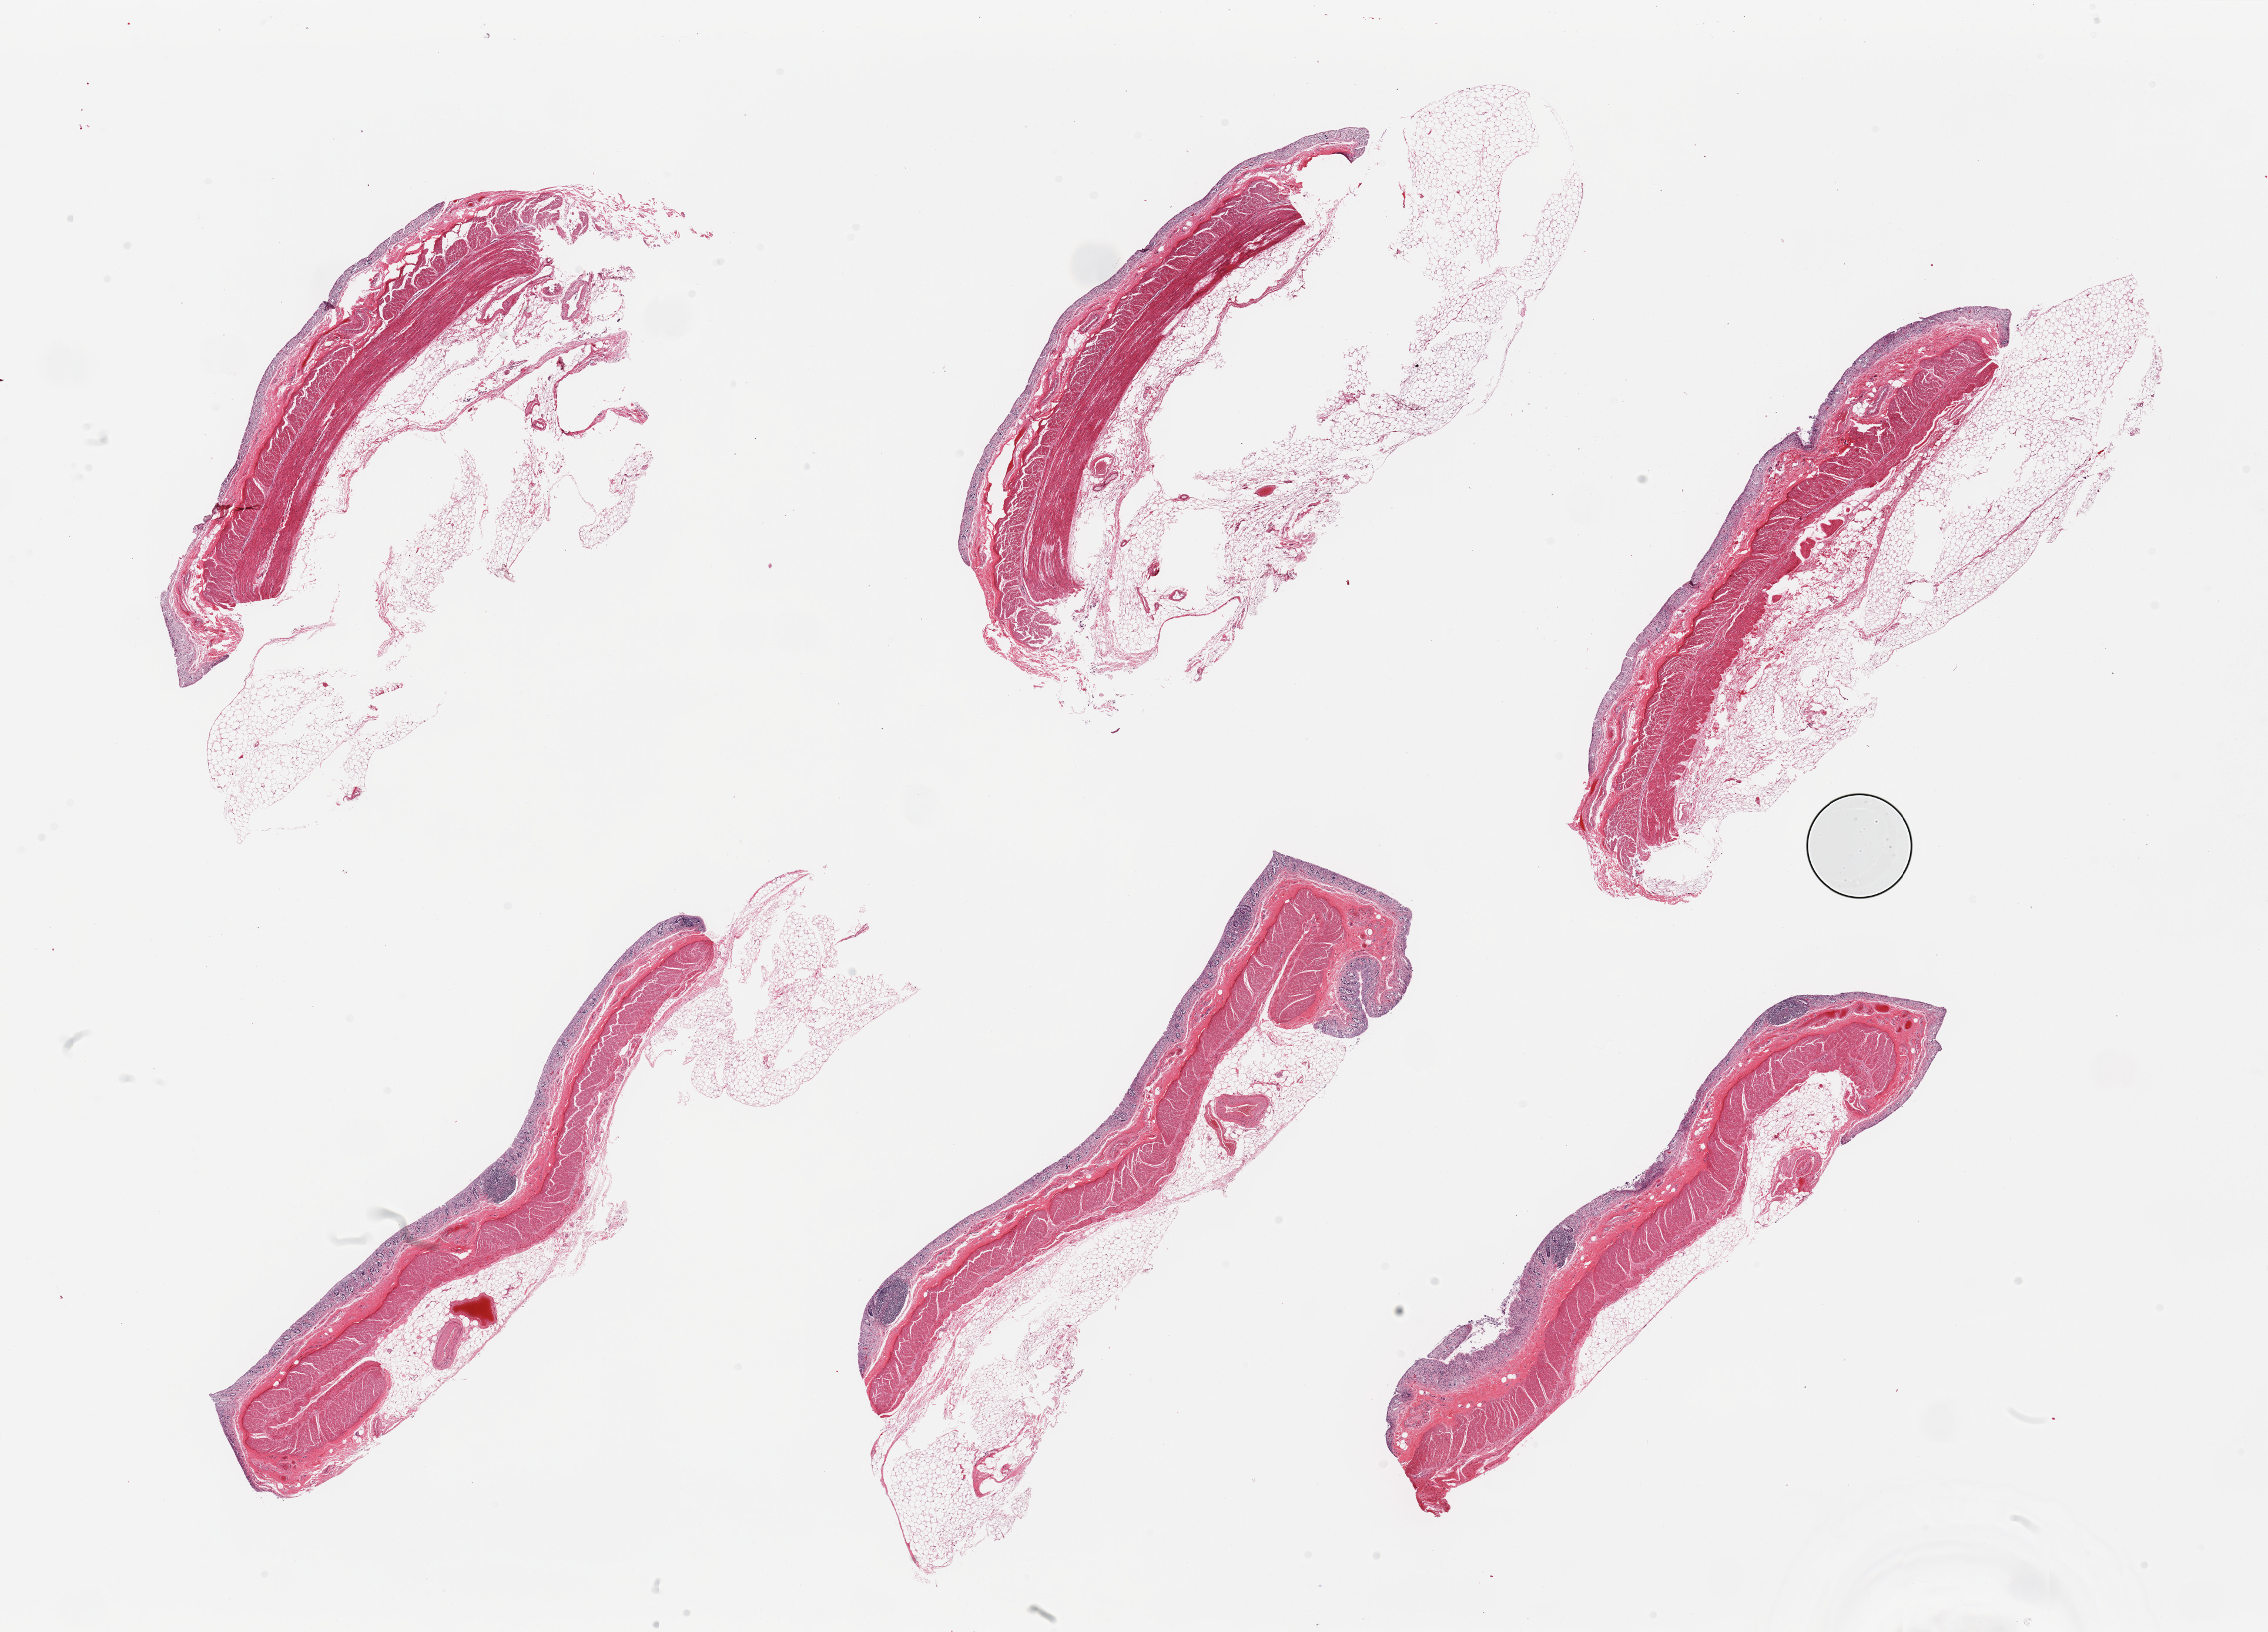
Whole-slide image, hematoxylin and eosin (H&E) stain, shown as a low-resolution overview of the whole scanned area (about 30.5 x 22.0 mm, acquisition: 20x scan). PAXgene-fixed paraffin-embedded (PFPE) section. Sampled site (target tissue): transverse colon. Tissue donor sample. Donor sex: male.
Review note (as recorded): 6 pieces; full thickness with attached fat, mucosa is severely autolyzed.